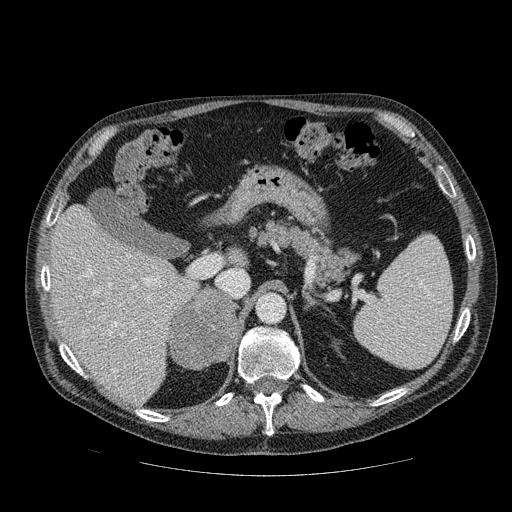
Contrast-enhanced abdominal CT, one axial slice; position 61 of 111 along the scan axis; 120 kVp; intravenous contrast given; soft-tissue window (W 400 / L 40 HU); 2.5 mm slice thickness; 512 × 512 image matrix. Patient: male, 56 years. From the clinical record (not read from this slice): diagnosis: adrenocortical carcinoma; tumour side: right adrenal; tumour size at pathology: 9 cm; Ki-67 index: 48 %; stage (as recorded): 4.
Outlined on this slice (semi-automatically segmented with operator editing):
- mass: box from (x=171, y=289) to (x=237, y=368) px